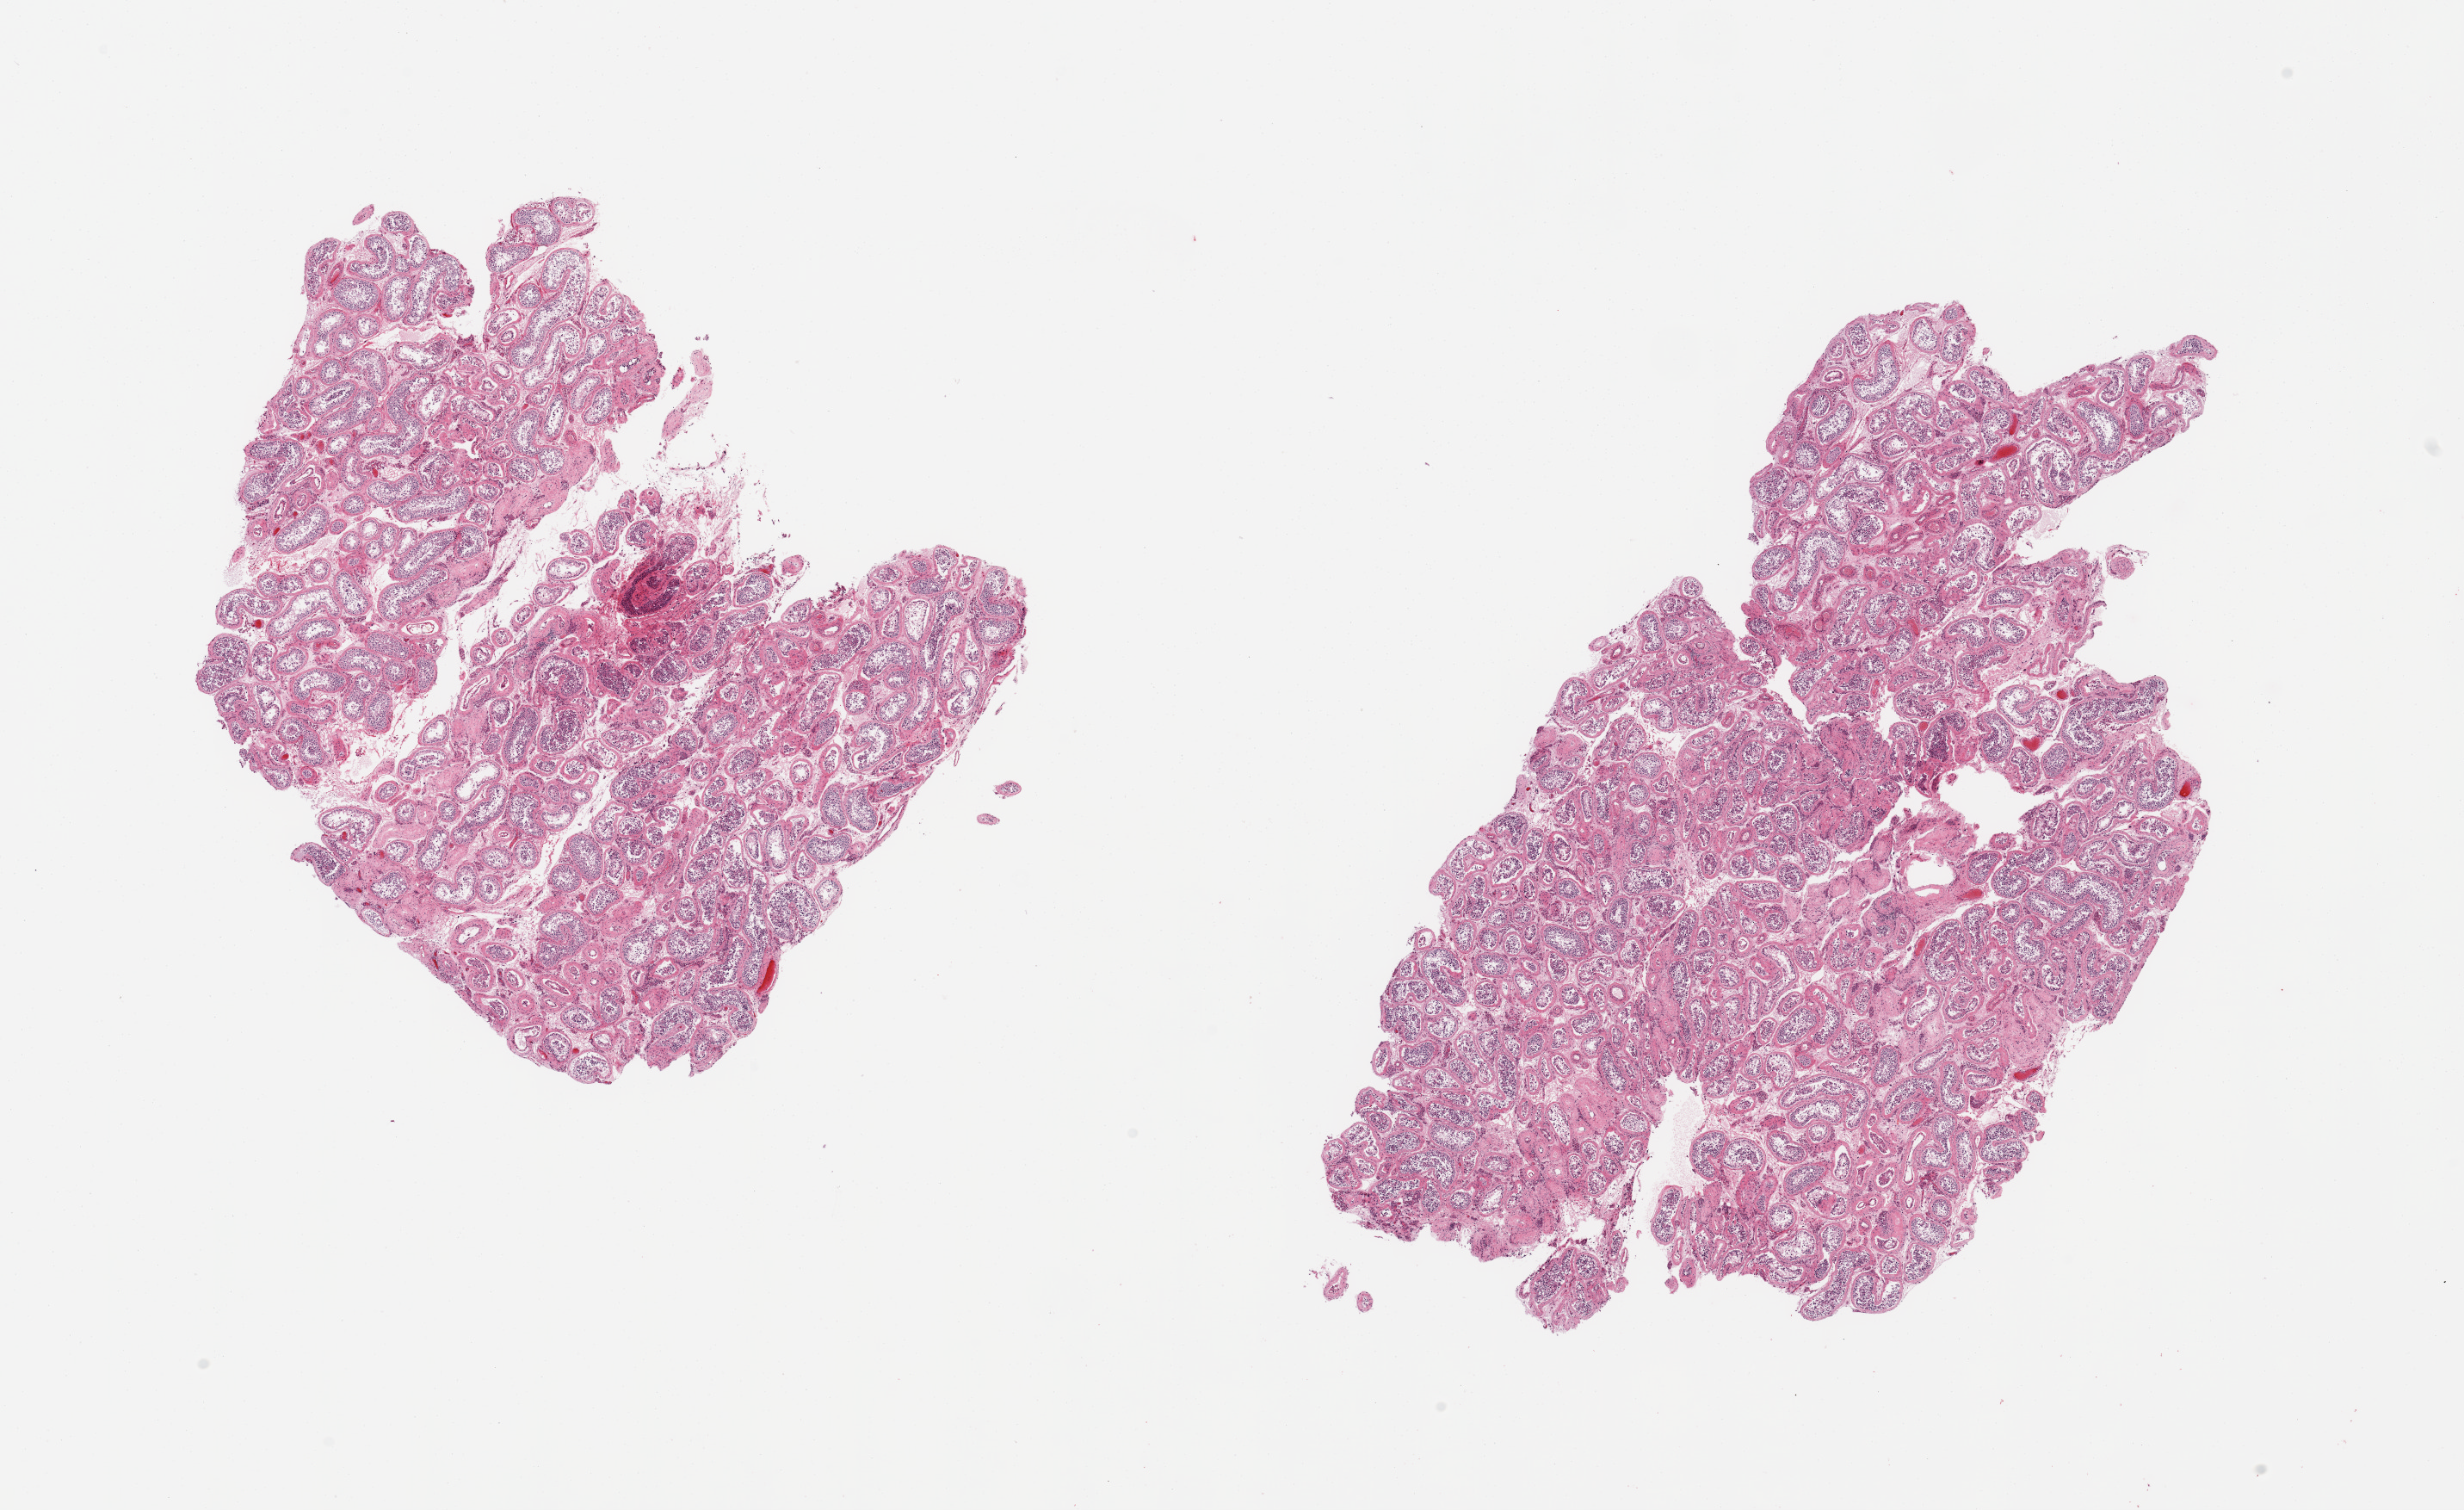
Digitized hematoxylin and eosin (H&E)-stained section, brightfield — low-resolution overview of the scanned area, about 22.6 x 13.9 mm (from a 20x scan); PAXgene-fixed, paraffin-embedded tissue; sampled site (target tissue): testis; tissue donor sample. Male donor.
- pathologist's review note for this sample: 2 pieces, markedly decreased spermatogenesis